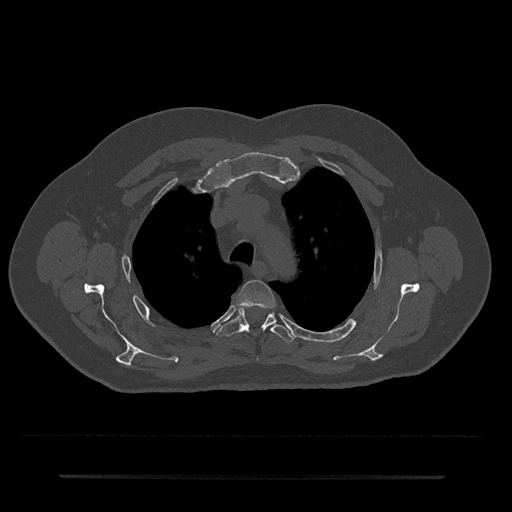
CT including the spine, one axial slice; slice 544 of 797 in the series (ordered by position); reconstruction kernel Br40s/3; 120 kVp; bone window (W 1800 / L 400 HU); 0.5 mm slice thickness; 512 × 512 image matrix. Male patient, age 69 years. Case-level facts recorded for this patient, not image findings: primary cancer: prostate.
Outlined on this slice (semi-automatic segmentation, software-assisted and operator-edited):
- T3 vertebra: bounding box [x1, y1, x2, y2] px = [237, 280, 276, 308]
- T4 vertebra: [217, 306, 294, 343]